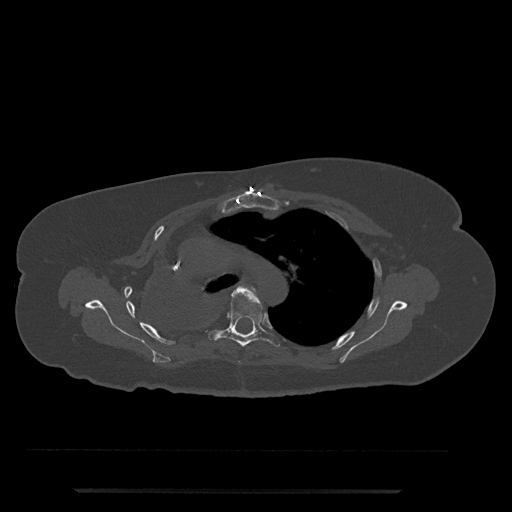
CT including the spine, one axial slice; slice 550 of 797 in the series (ordered by position); reconstruction kernel Br40s/3; 120 kVp; bone window (W 1800 / L 400 HU); 0.5 mm slice thickness; 512 × 512 image matrix. Patient: female, 51 years. Case-level facts recorded for this patient, not image findings: primary cancer: neuro.
Annotated regions visible in this slice (semi-automatically segmented with operator editing):
- T5 vertebra: box from (x=208, y=287) to (x=280, y=347) px